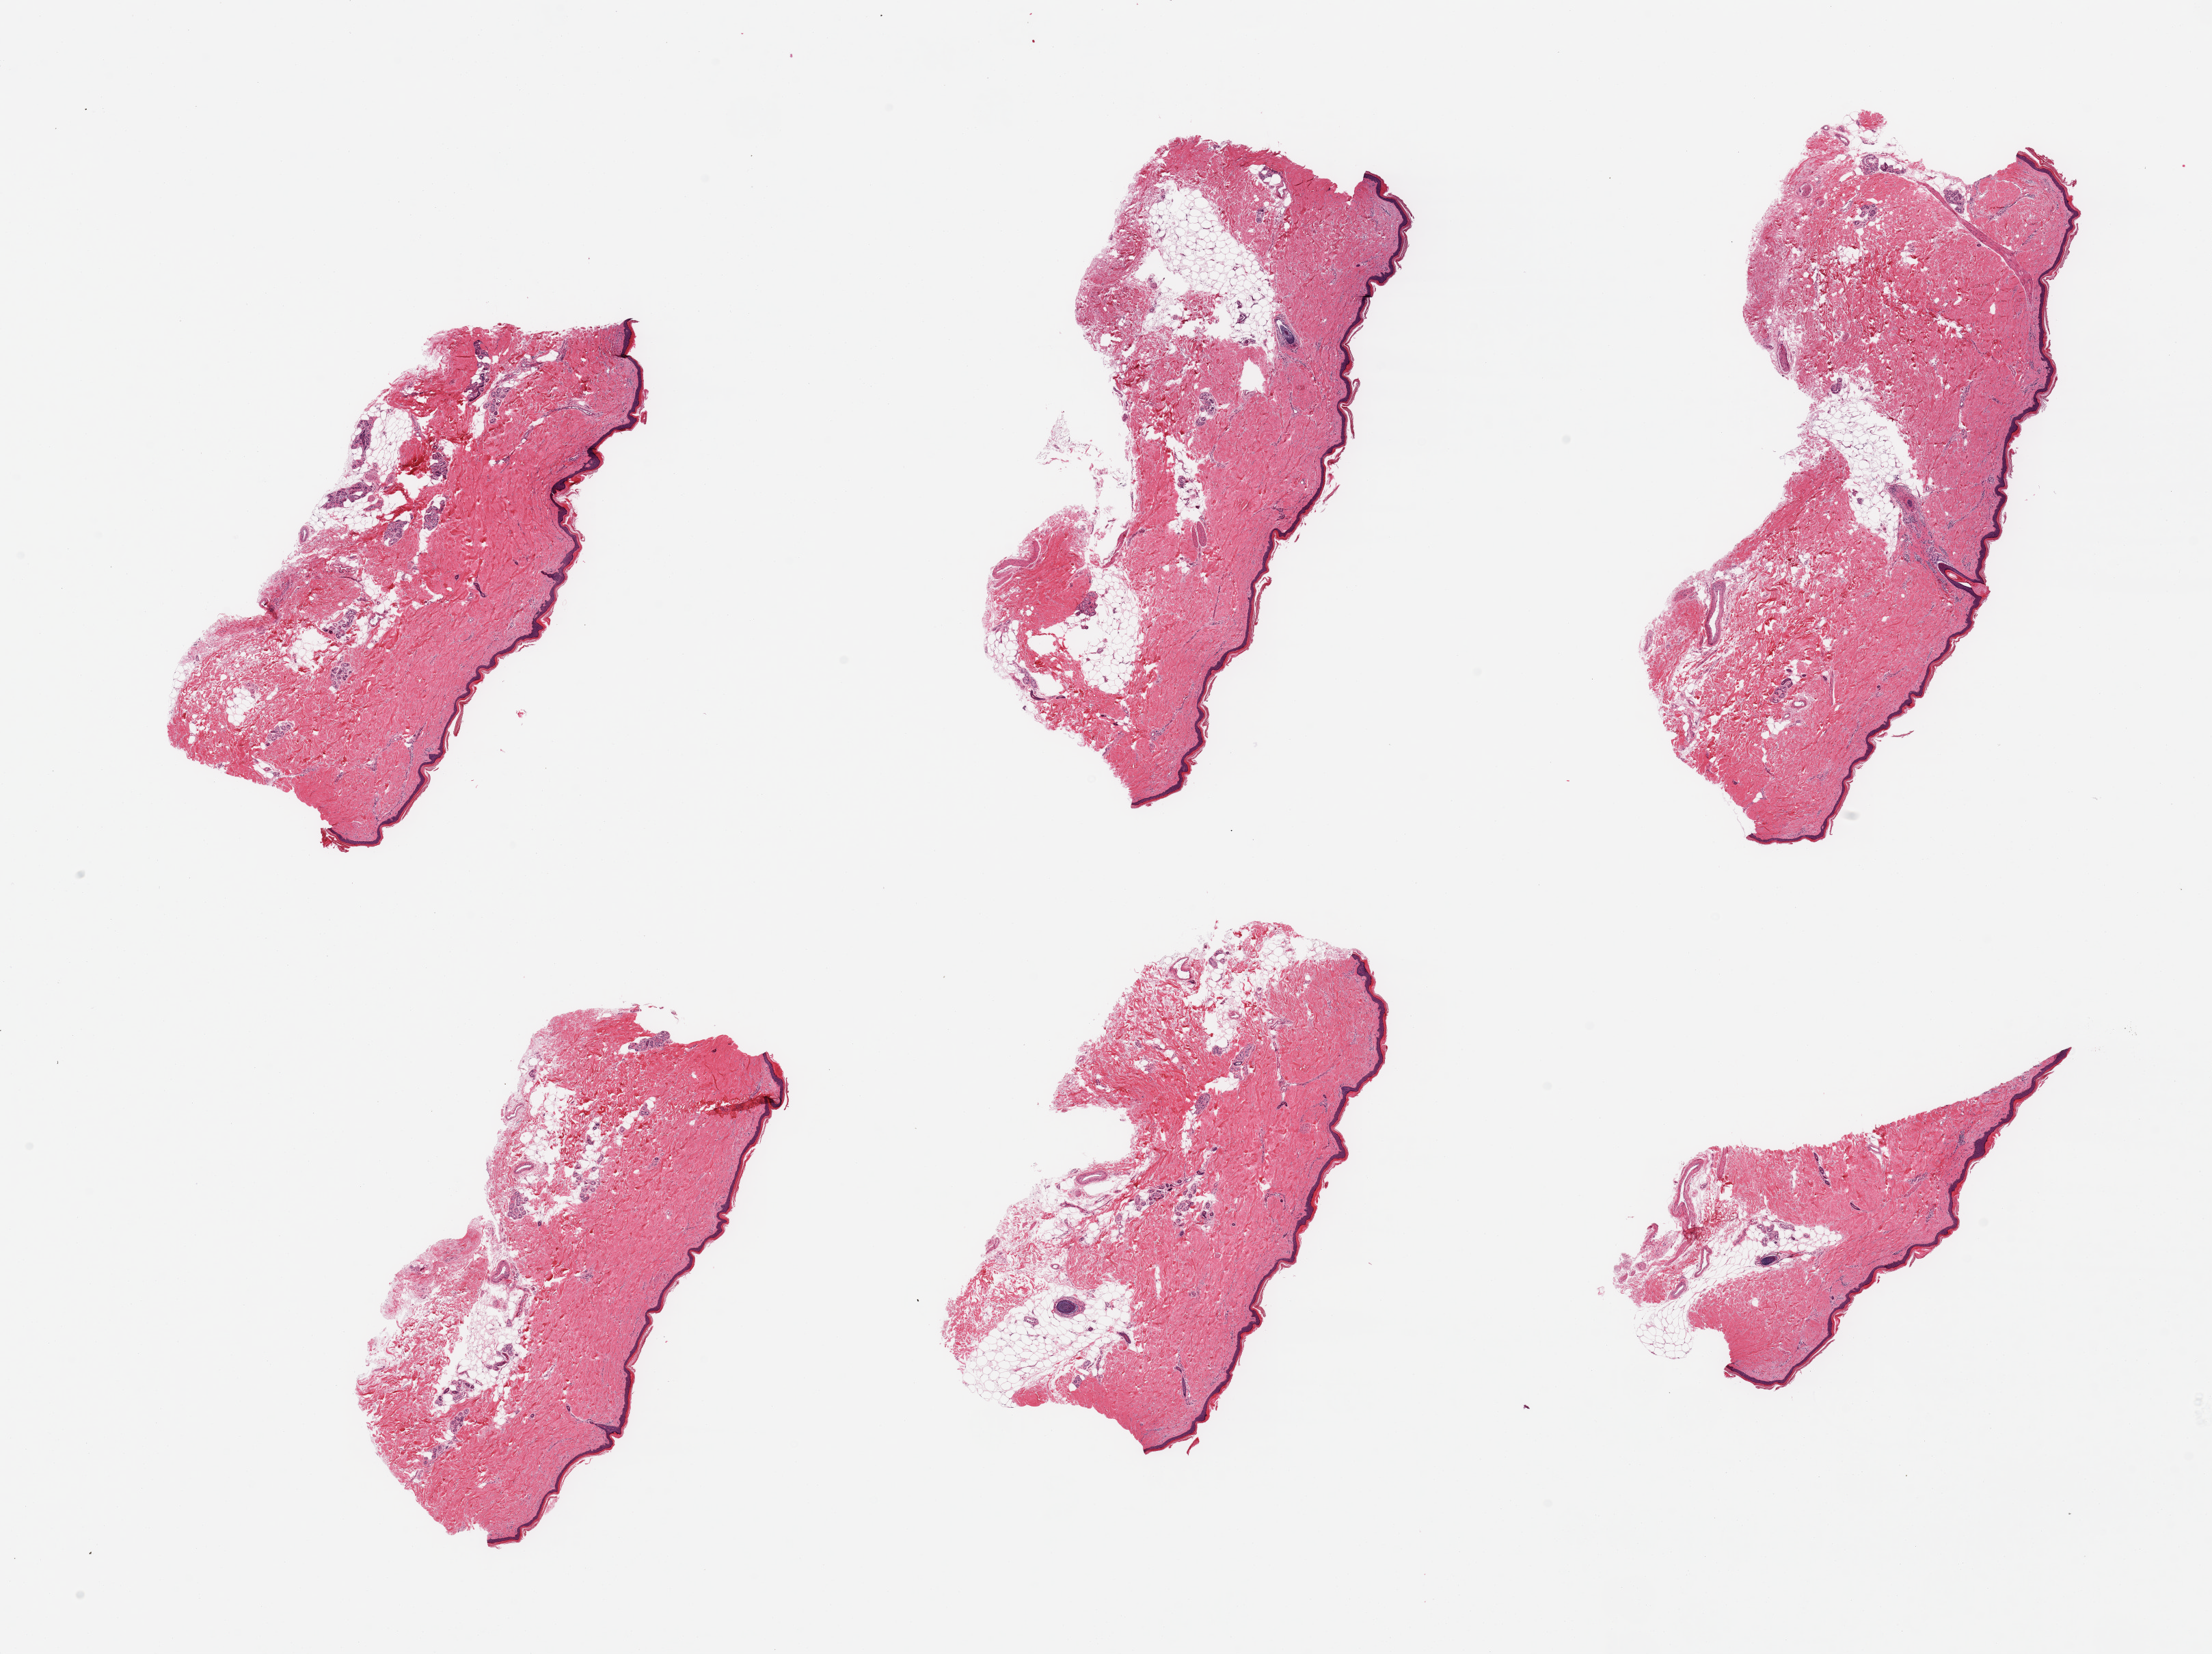
Hematoxylin and eosin (H&E) whole-slide image, brightfield, whole scanned area (about 25.6 x 19.1 mm, acquisition: 20x scan) shown as a low-resolution overview, PAXgene-fixed paraffin-embedded (PFPE) section, section of skin of lower leg (target tissue), donor tissue sample. Male donor.
Pathologist's review note for this sample: 6 pieces, trace dermal fat; squamous epithelium is ~40-50 microns.